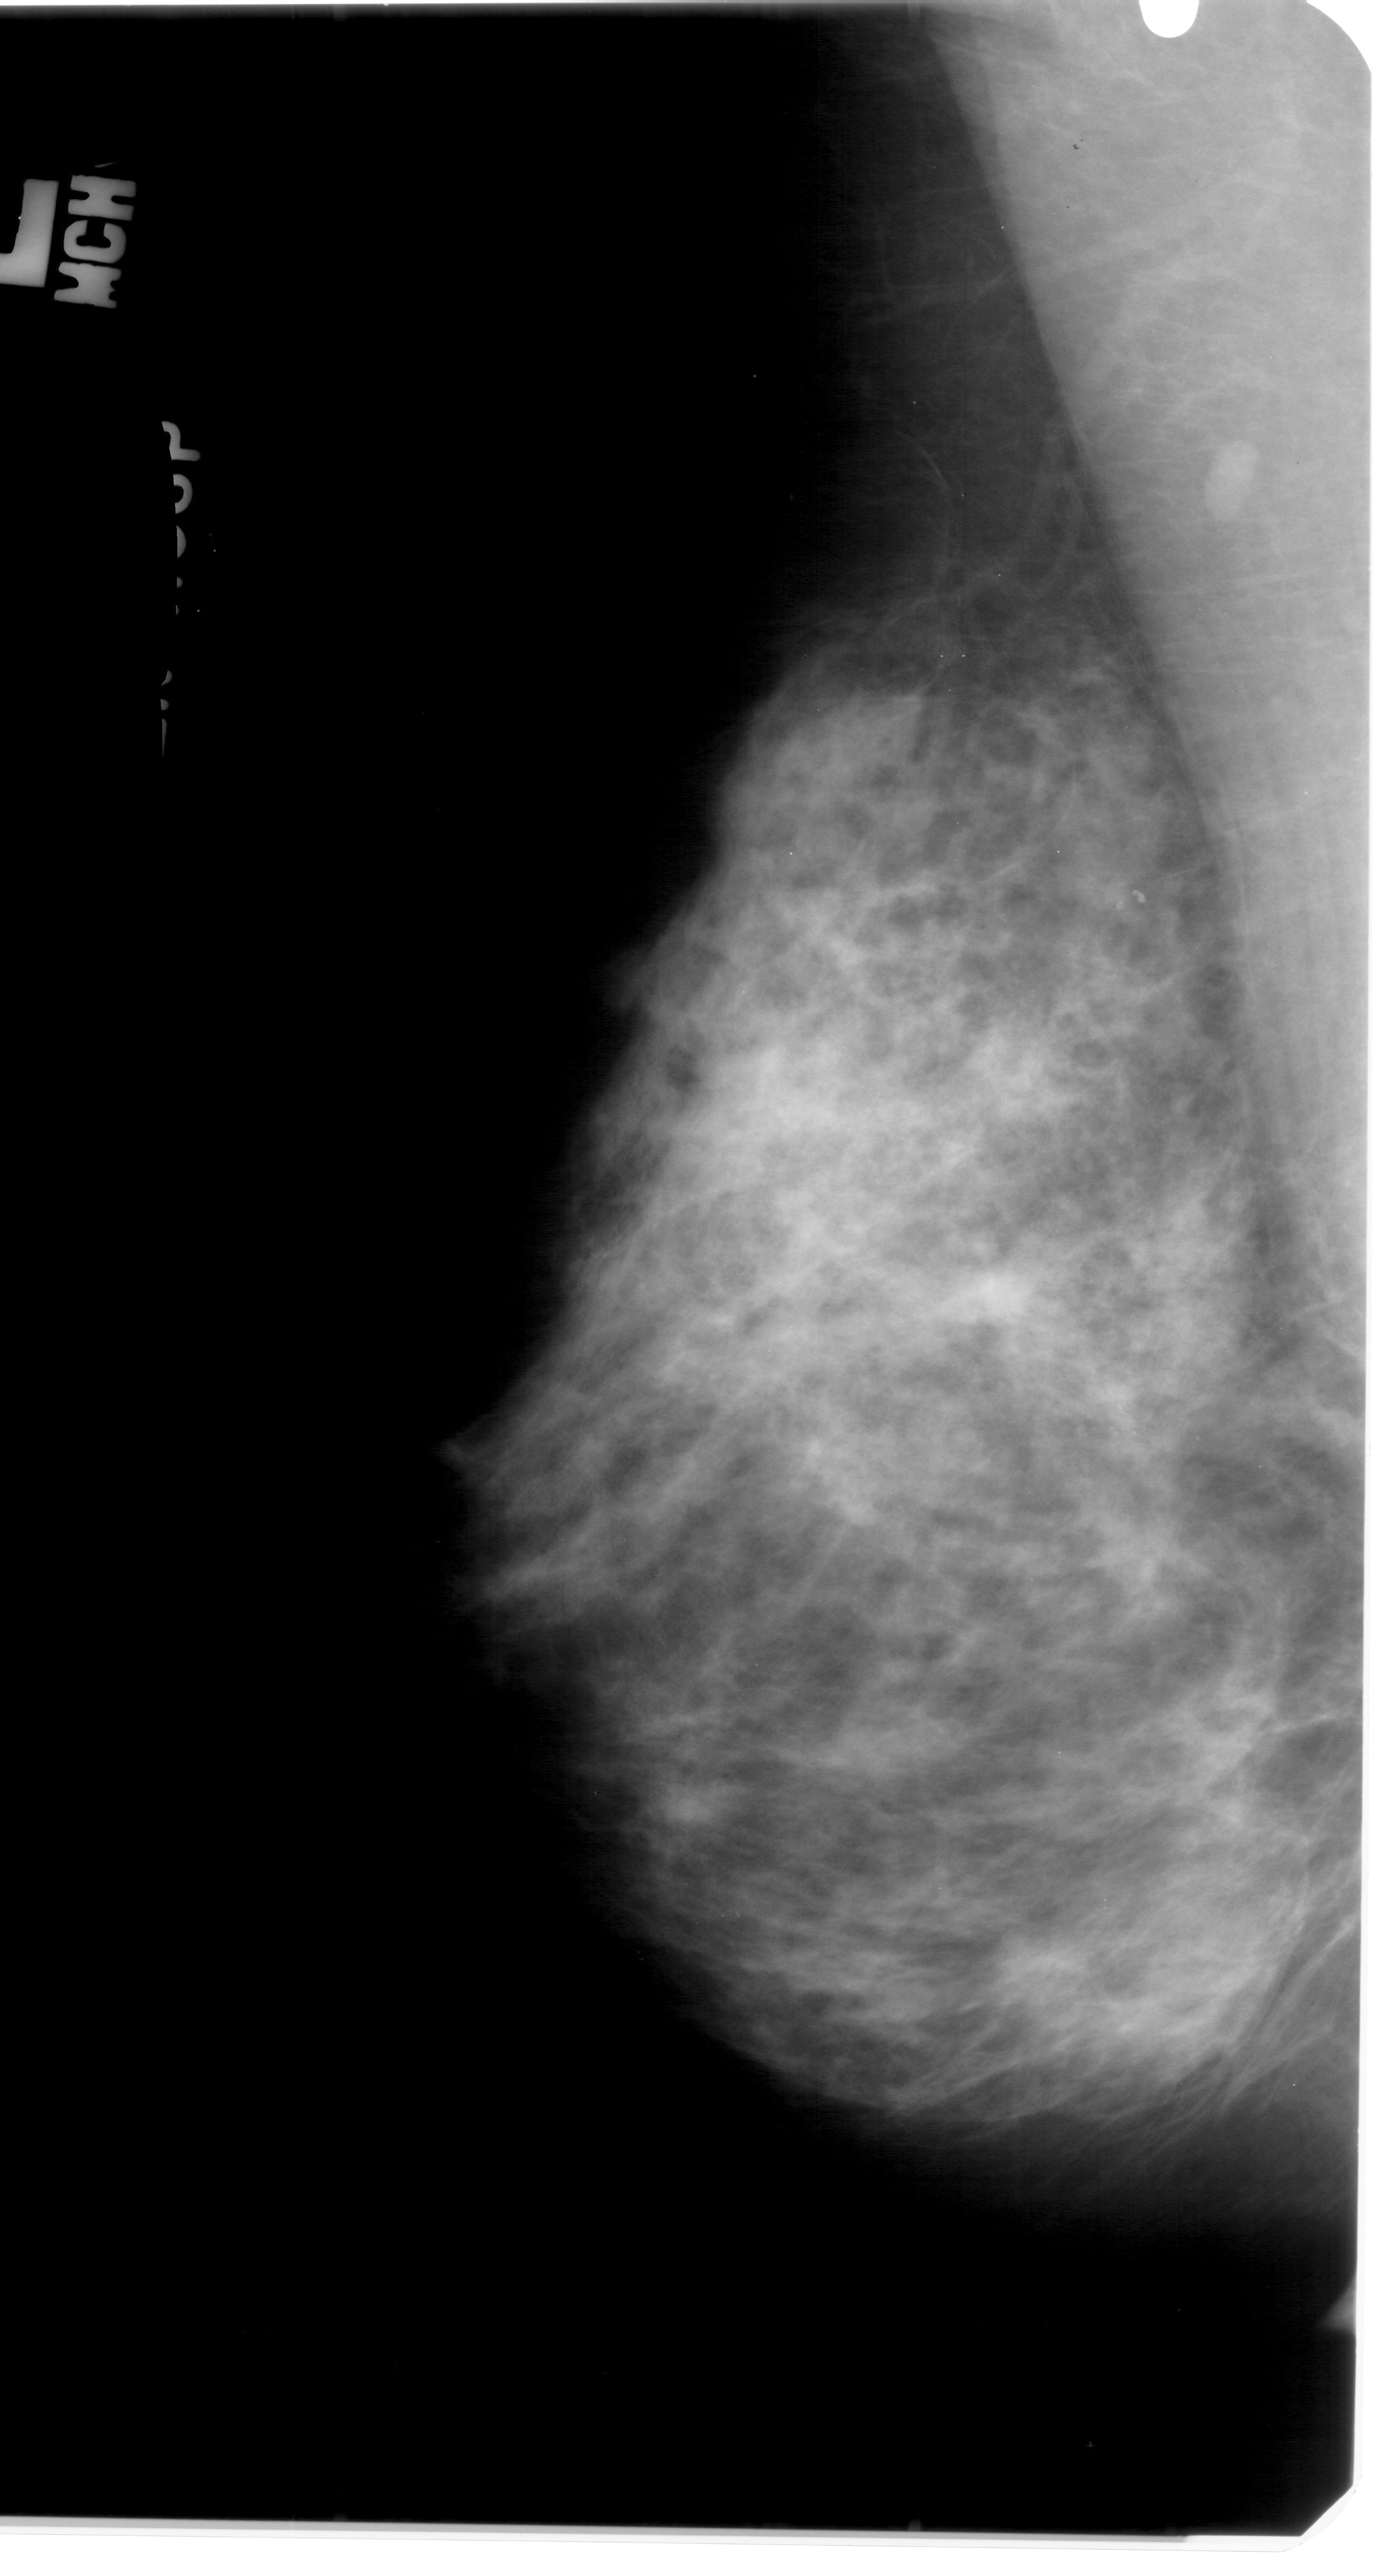
Scanned film-screen mammogram; left breast; mediolateral oblique (MLO) view; BI-RADS breast density category 3 (scale 1–4).
Abnormality record for this image: calcifications, morphology pleomorphic, distribution clustered; BI-RADS assessment category 4; pathology result (as recorded, not read from the image): benign.